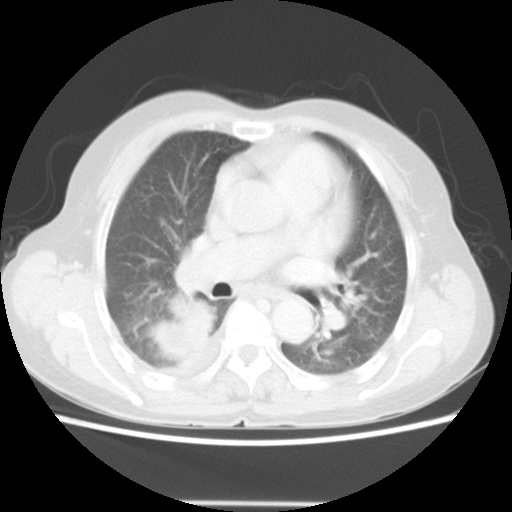
Chest CT, one axial slice; position 29 of 52 along the scan axis; reconstruction kernel STANDARD; 140 kVp; lung window (W 1500 / L -600 HU); 5 mm slice thickness; 512 × 512 image matrix, field of view 337 × 337 mm. Female patient, age 67 years. From the clinical record (not read from this slice): clinical TNM (as recorded): T3 N1 M1.
Structures marked on this image (rectangle marked by the reading radiologist):
- lung tumour (recorded histology: adenocarcinoma): bounding box <146,290,217,368> (left, top, right, bottom; pixels)